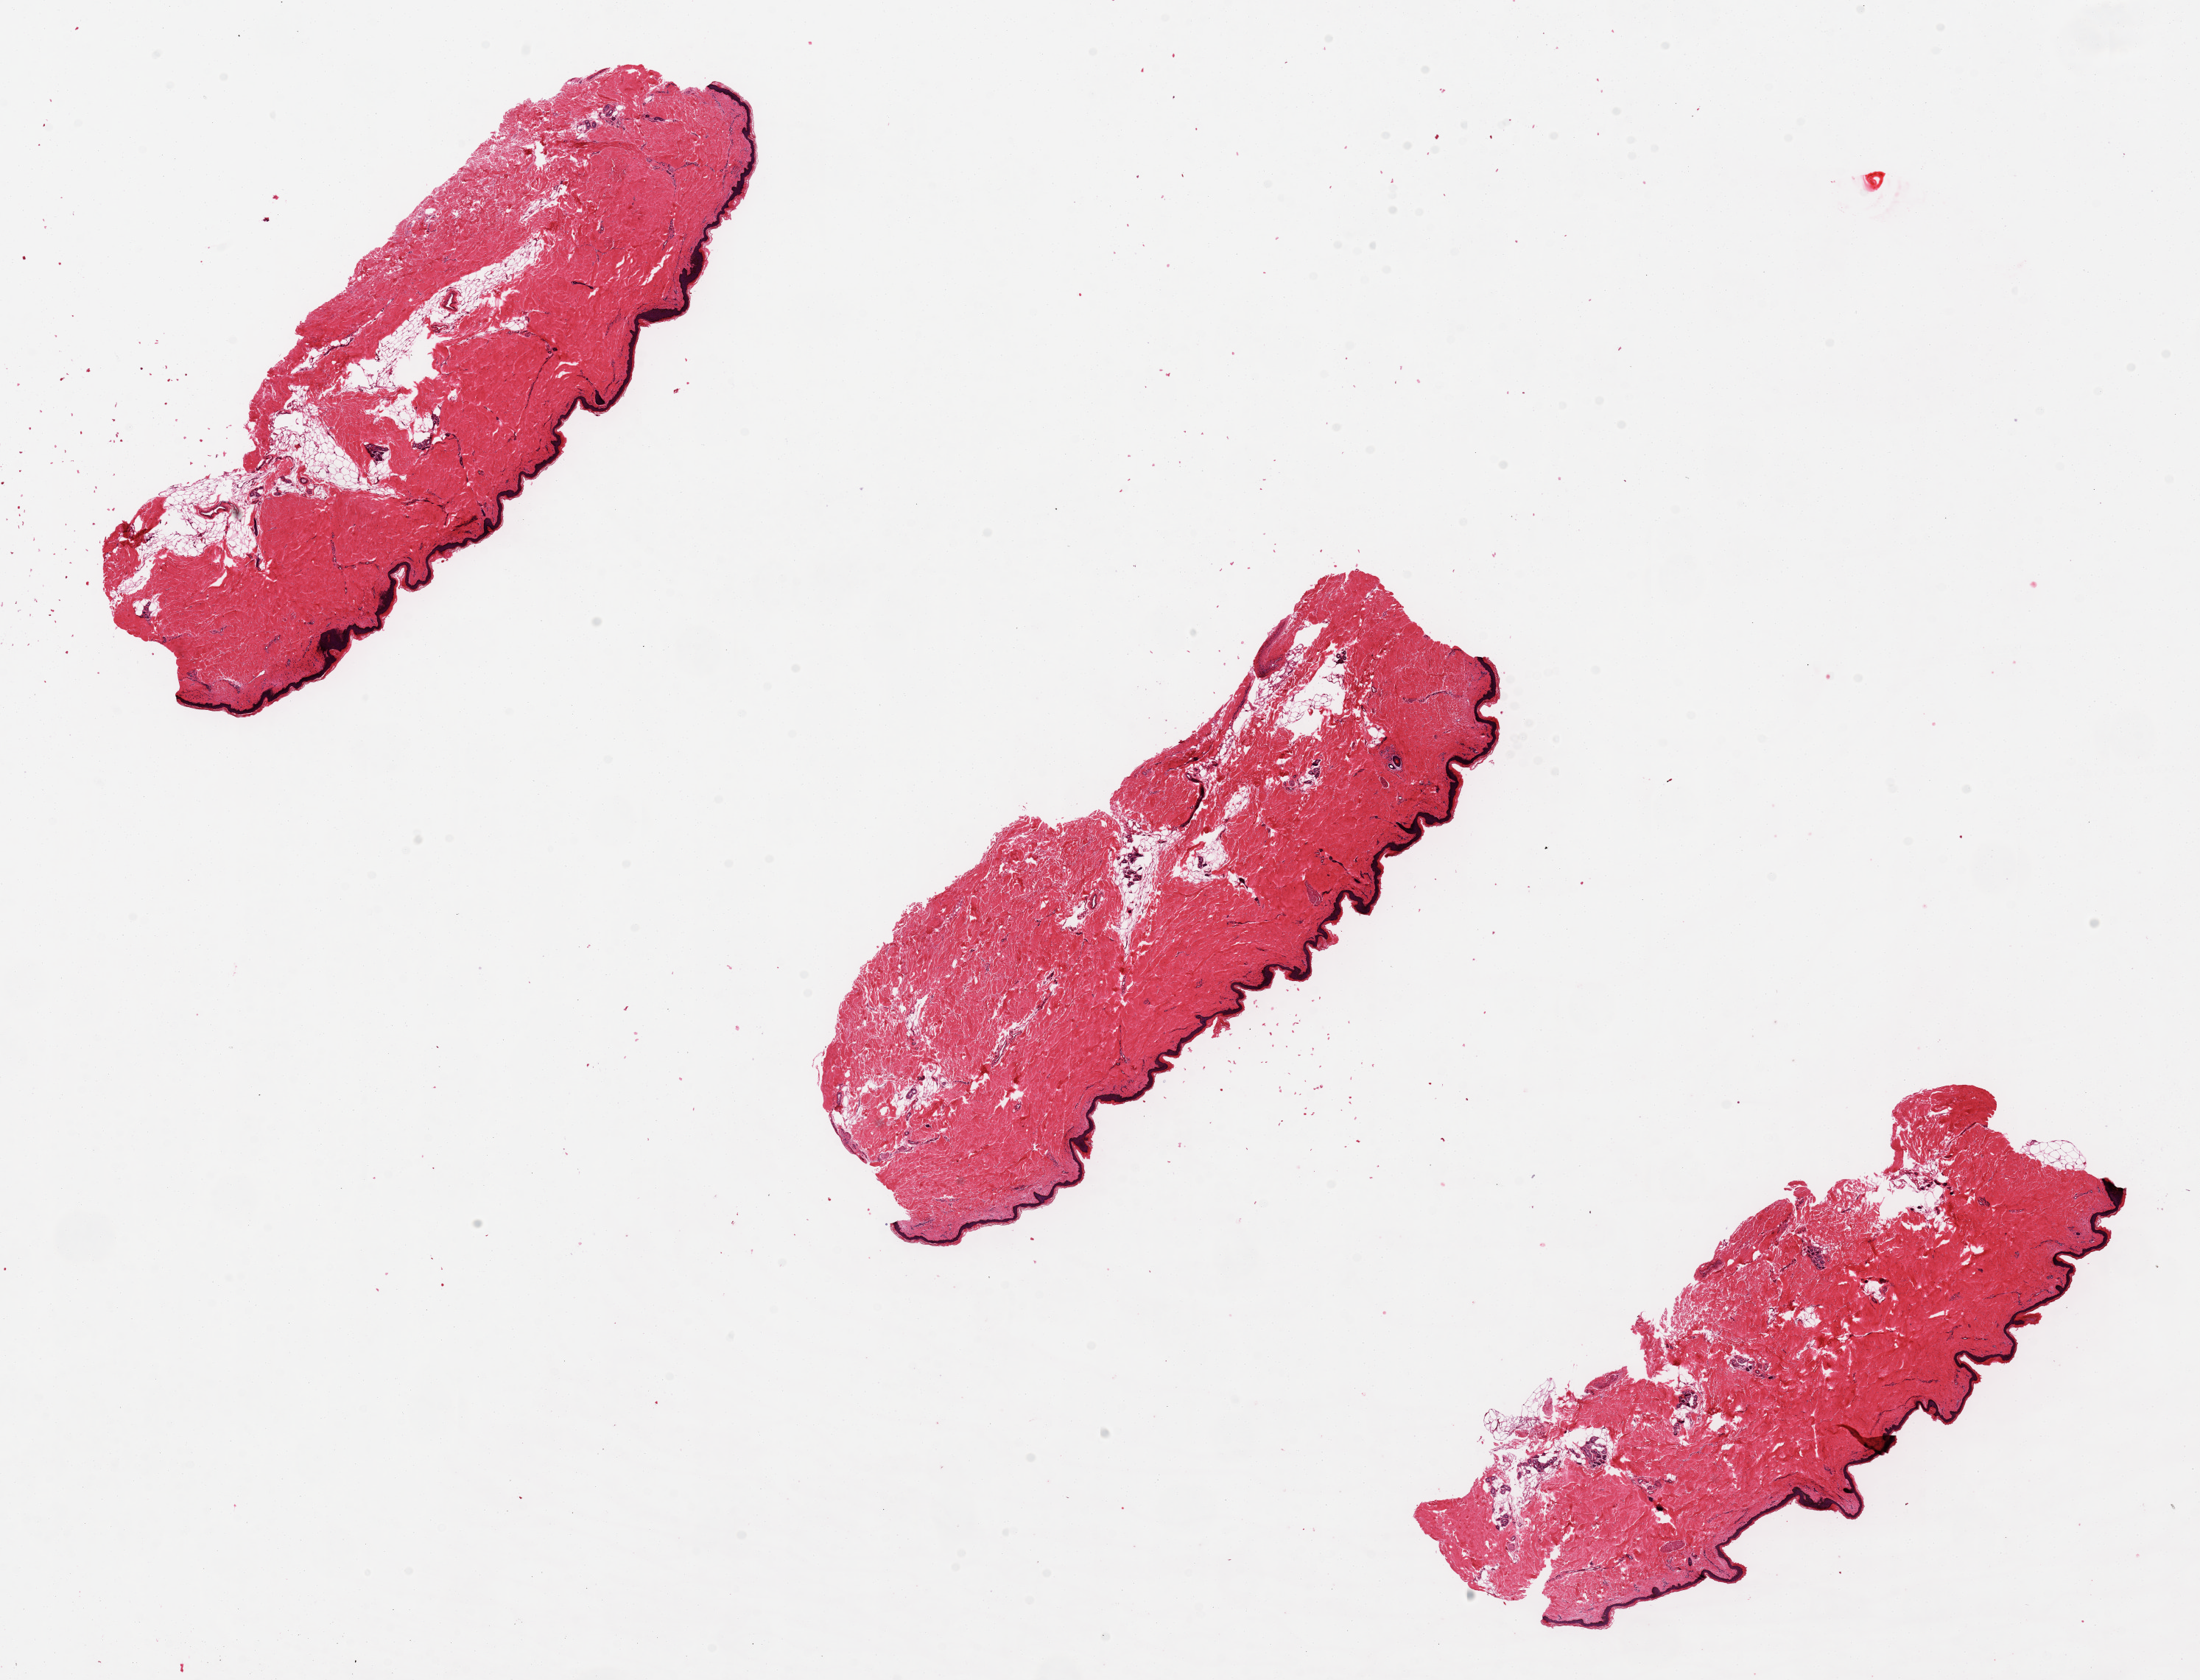
Haematoxylin and eosin whole-slide image, low-resolution overview of the scanned area, about 23.6 x 18.0 mm (from a 20x scan); PAXgene-fixed paraffin-embedded (PFPE) section; target tissue: skin of lower leg; donor tissue sample.
Review note (as recorded): Epidermis is ~2-3% of specimen thickness. Patchy areas of soft tissue (deep) are poorly fixed.